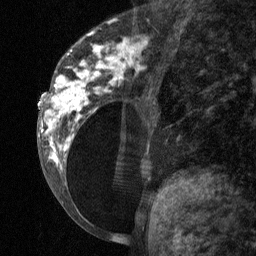
Breast MRI (dynamic contrast-enhanced), one sagittal slice. Slice 26 of 64 in the series (ordered by position). Dynamic contrast-enhanced study with each time point stored as its own series, time point 2 of 3 at this slice position (early post-contrast, ordered by acquisition time). 1.5 T. TE 4.8 ms, TR 27 ms. 2 mm slice thickness. 256 × 256 image matrix, field of view 180 × 180 mm. Patient: female, 34 years. Case-level facts recorded for this patient, not image findings: setting: breast cancer imaged before/during neoadjuvant chemotherapy; receptor status: HR-positive, HER2-negative.
Annotated regions visible in this slice (semi-automatic segmentation, software-assisted and operator-edited):
- analysis volume of interest (the breast-tissue region the enhancement analysis was run in; not a lesion): box from (x=41, y=23) to (x=157, y=197) px
- tumour enhancement mask (voxels above the 90 % enhancement threshold inside the analysis volume of interest): (x=41, y=31)–(x=144, y=170)